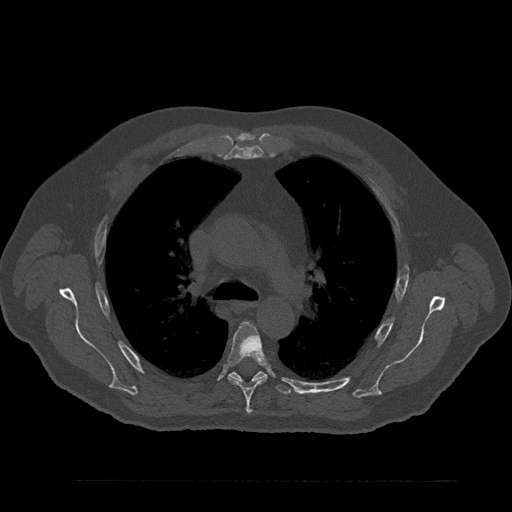
CT including the spine, one axial slice. Position 590 of 797 along the scan axis. Bone window (W 1800 / L 400 HU). 0.5 mm slice thickness. 512 × 512 image matrix, field of view 430 × 430 mm. Patient: male, 61 years. From the clinical record (not read from this slice): primary cancer: prostate.
Annotated regions visible in this slice (semi-automatically segmented with operator editing):
- T5 vertebra: bounding box (x1, y1, x2, y2) in pixels: (227, 322, 267, 414)
- T6 vertebra: (228, 364, 291, 394)